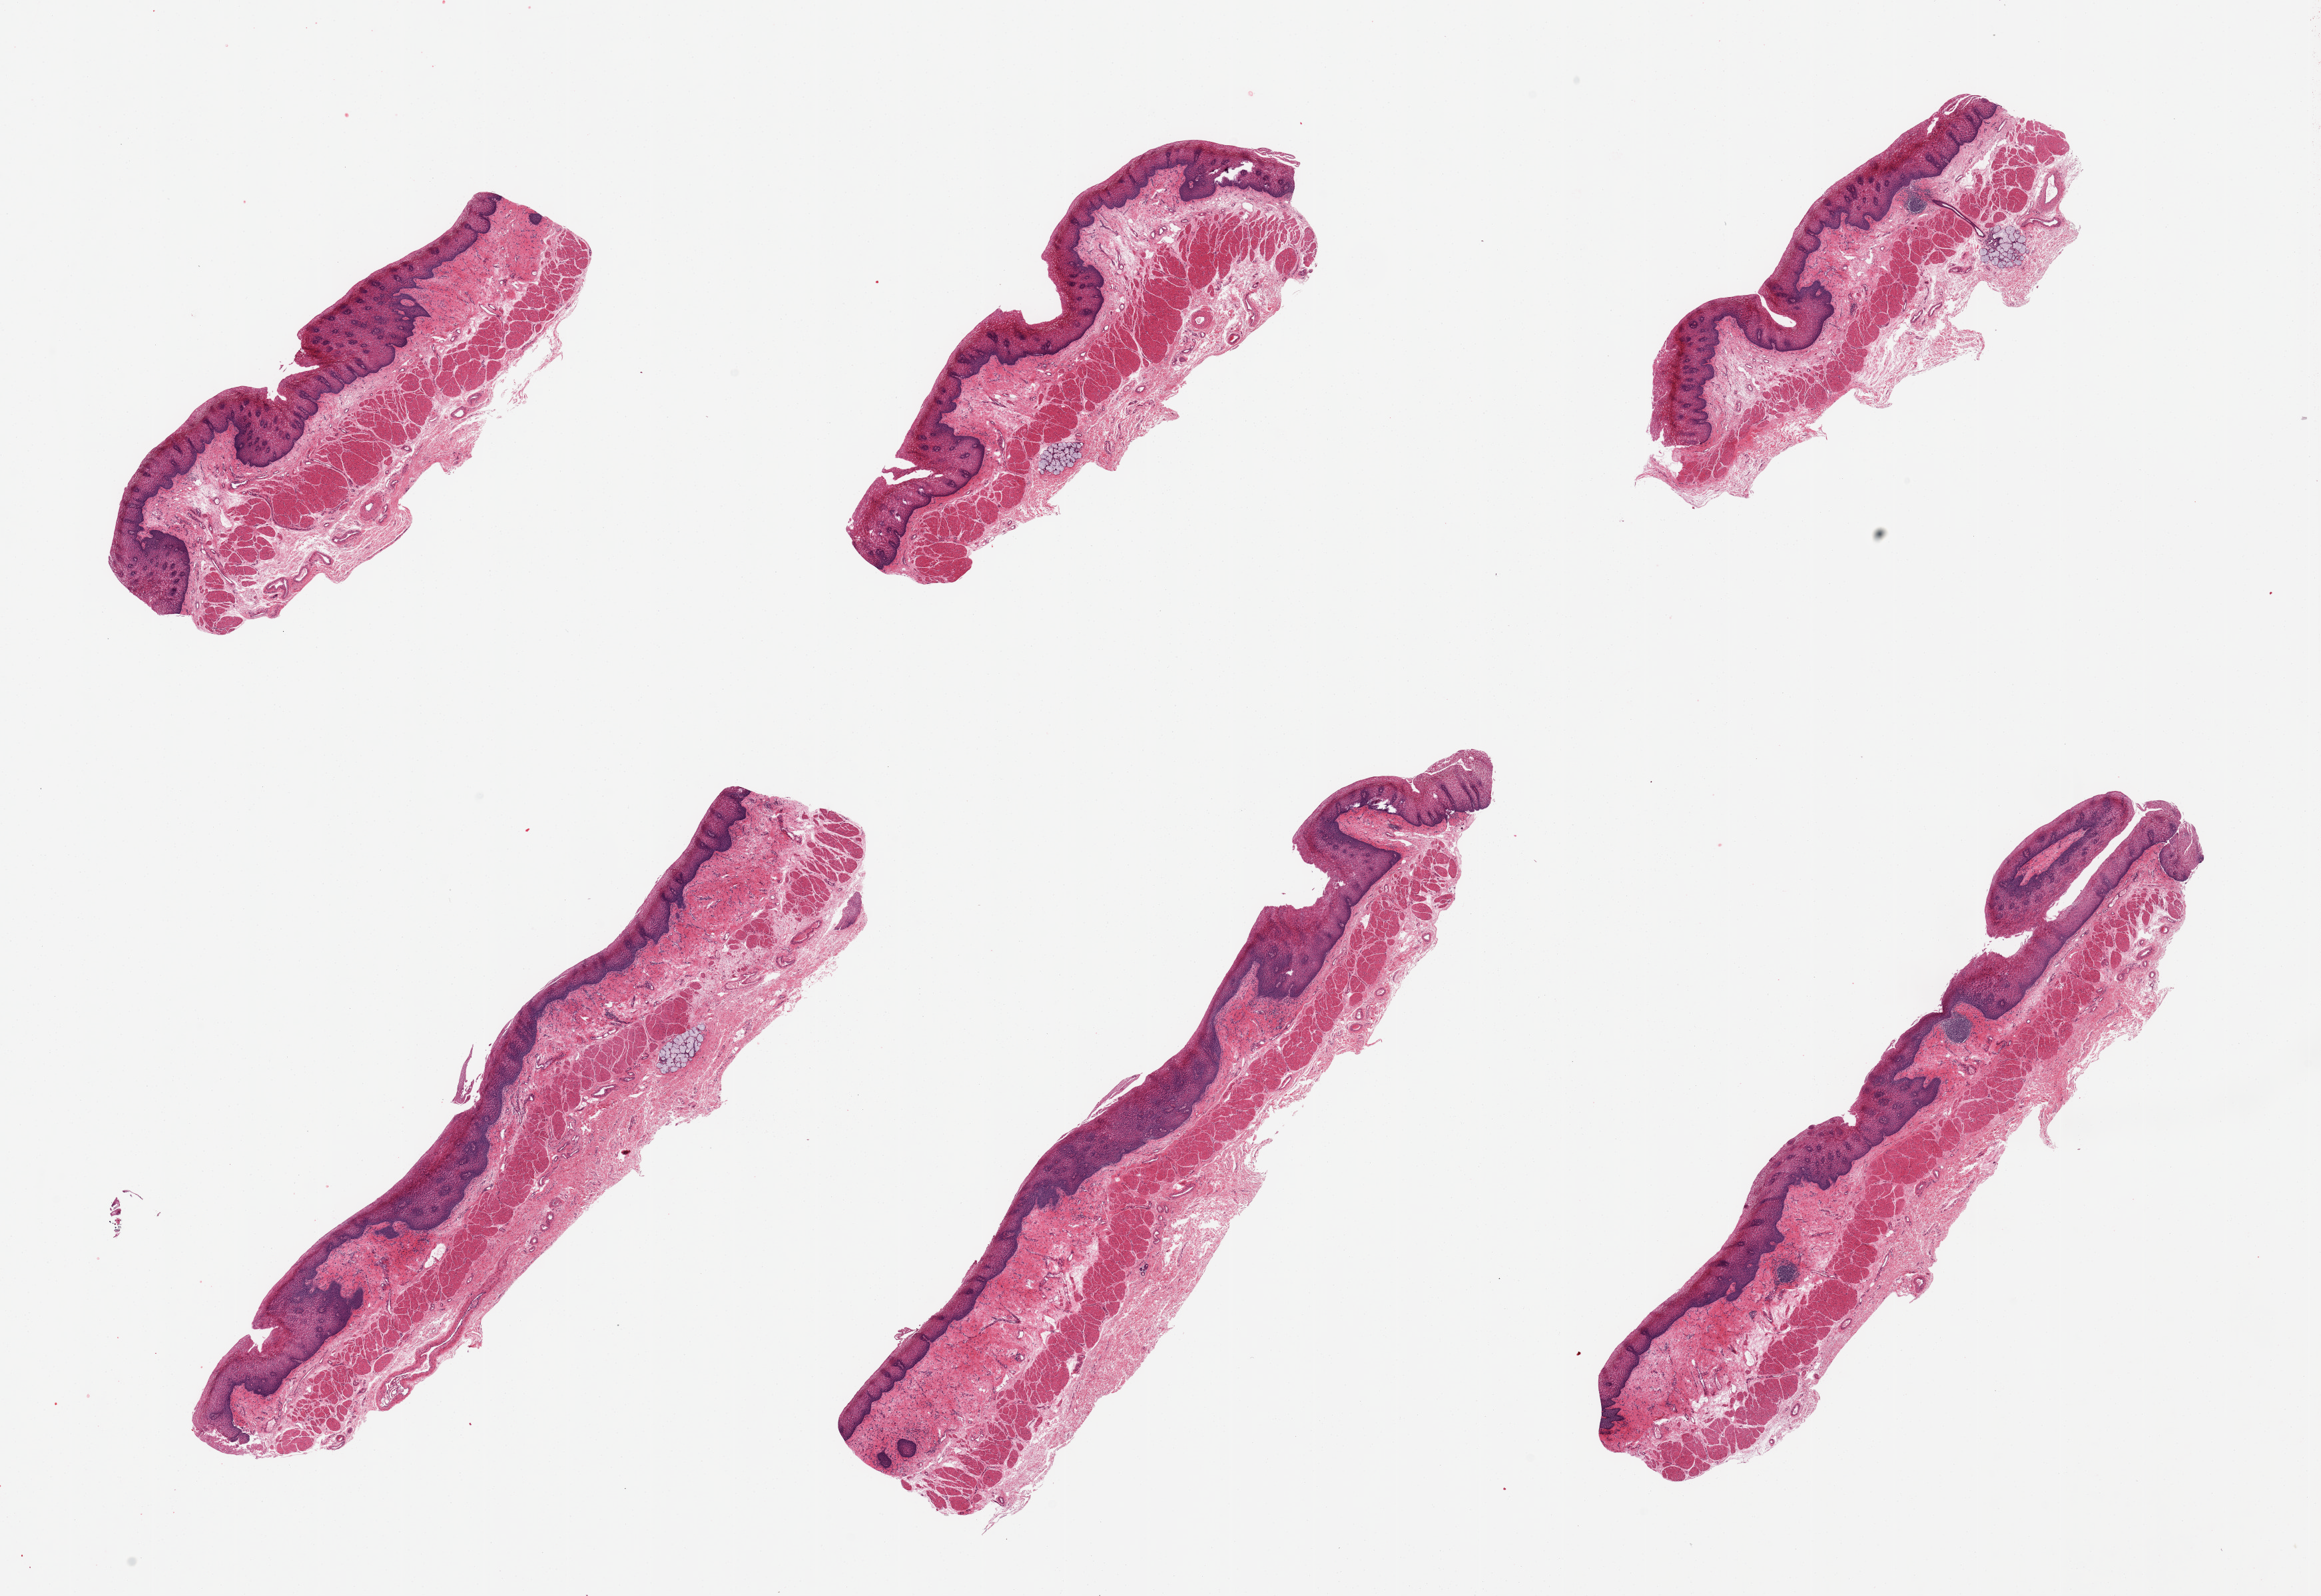
Hematoxylin and eosin (H&E) whole-slide image — a low-resolution overview of the entire scanned area, about 27.6 x 19.0 mm (acquisition: 20x scan); PAXgene-fixed, paraffin-embedded tissue; target tissue: esophageal mucous membrane; tissue donor sample. Donor sex: female.
Pathologist's review note for this sample: 6 pieces, squamous mucosa up to ~0.6mm, ~30-40% thickness.